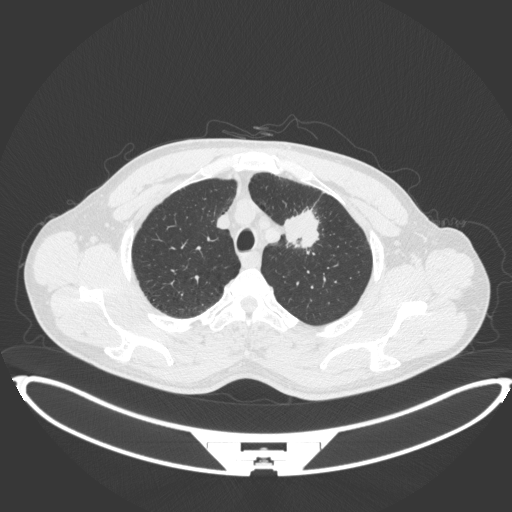
Chest CT, one axial slice; slice 359 of 407 in the series (ordered by position); reconstruction kernel B31f; 120 kVp; lung window (W 1500 / L -600 HU); 512 × 512 image matrix. Male patient, age 60 years. From the clinical record (not read from this slice): clinical TNM (as recorded): T2a N0 M0.
Outlined on this slice (rectangle marked by the reading radiologist):
- lung tumour (recorded histology: squamous cell carcinoma): bounding box <284,207,322,251> (left, top, right, bottom; pixels)